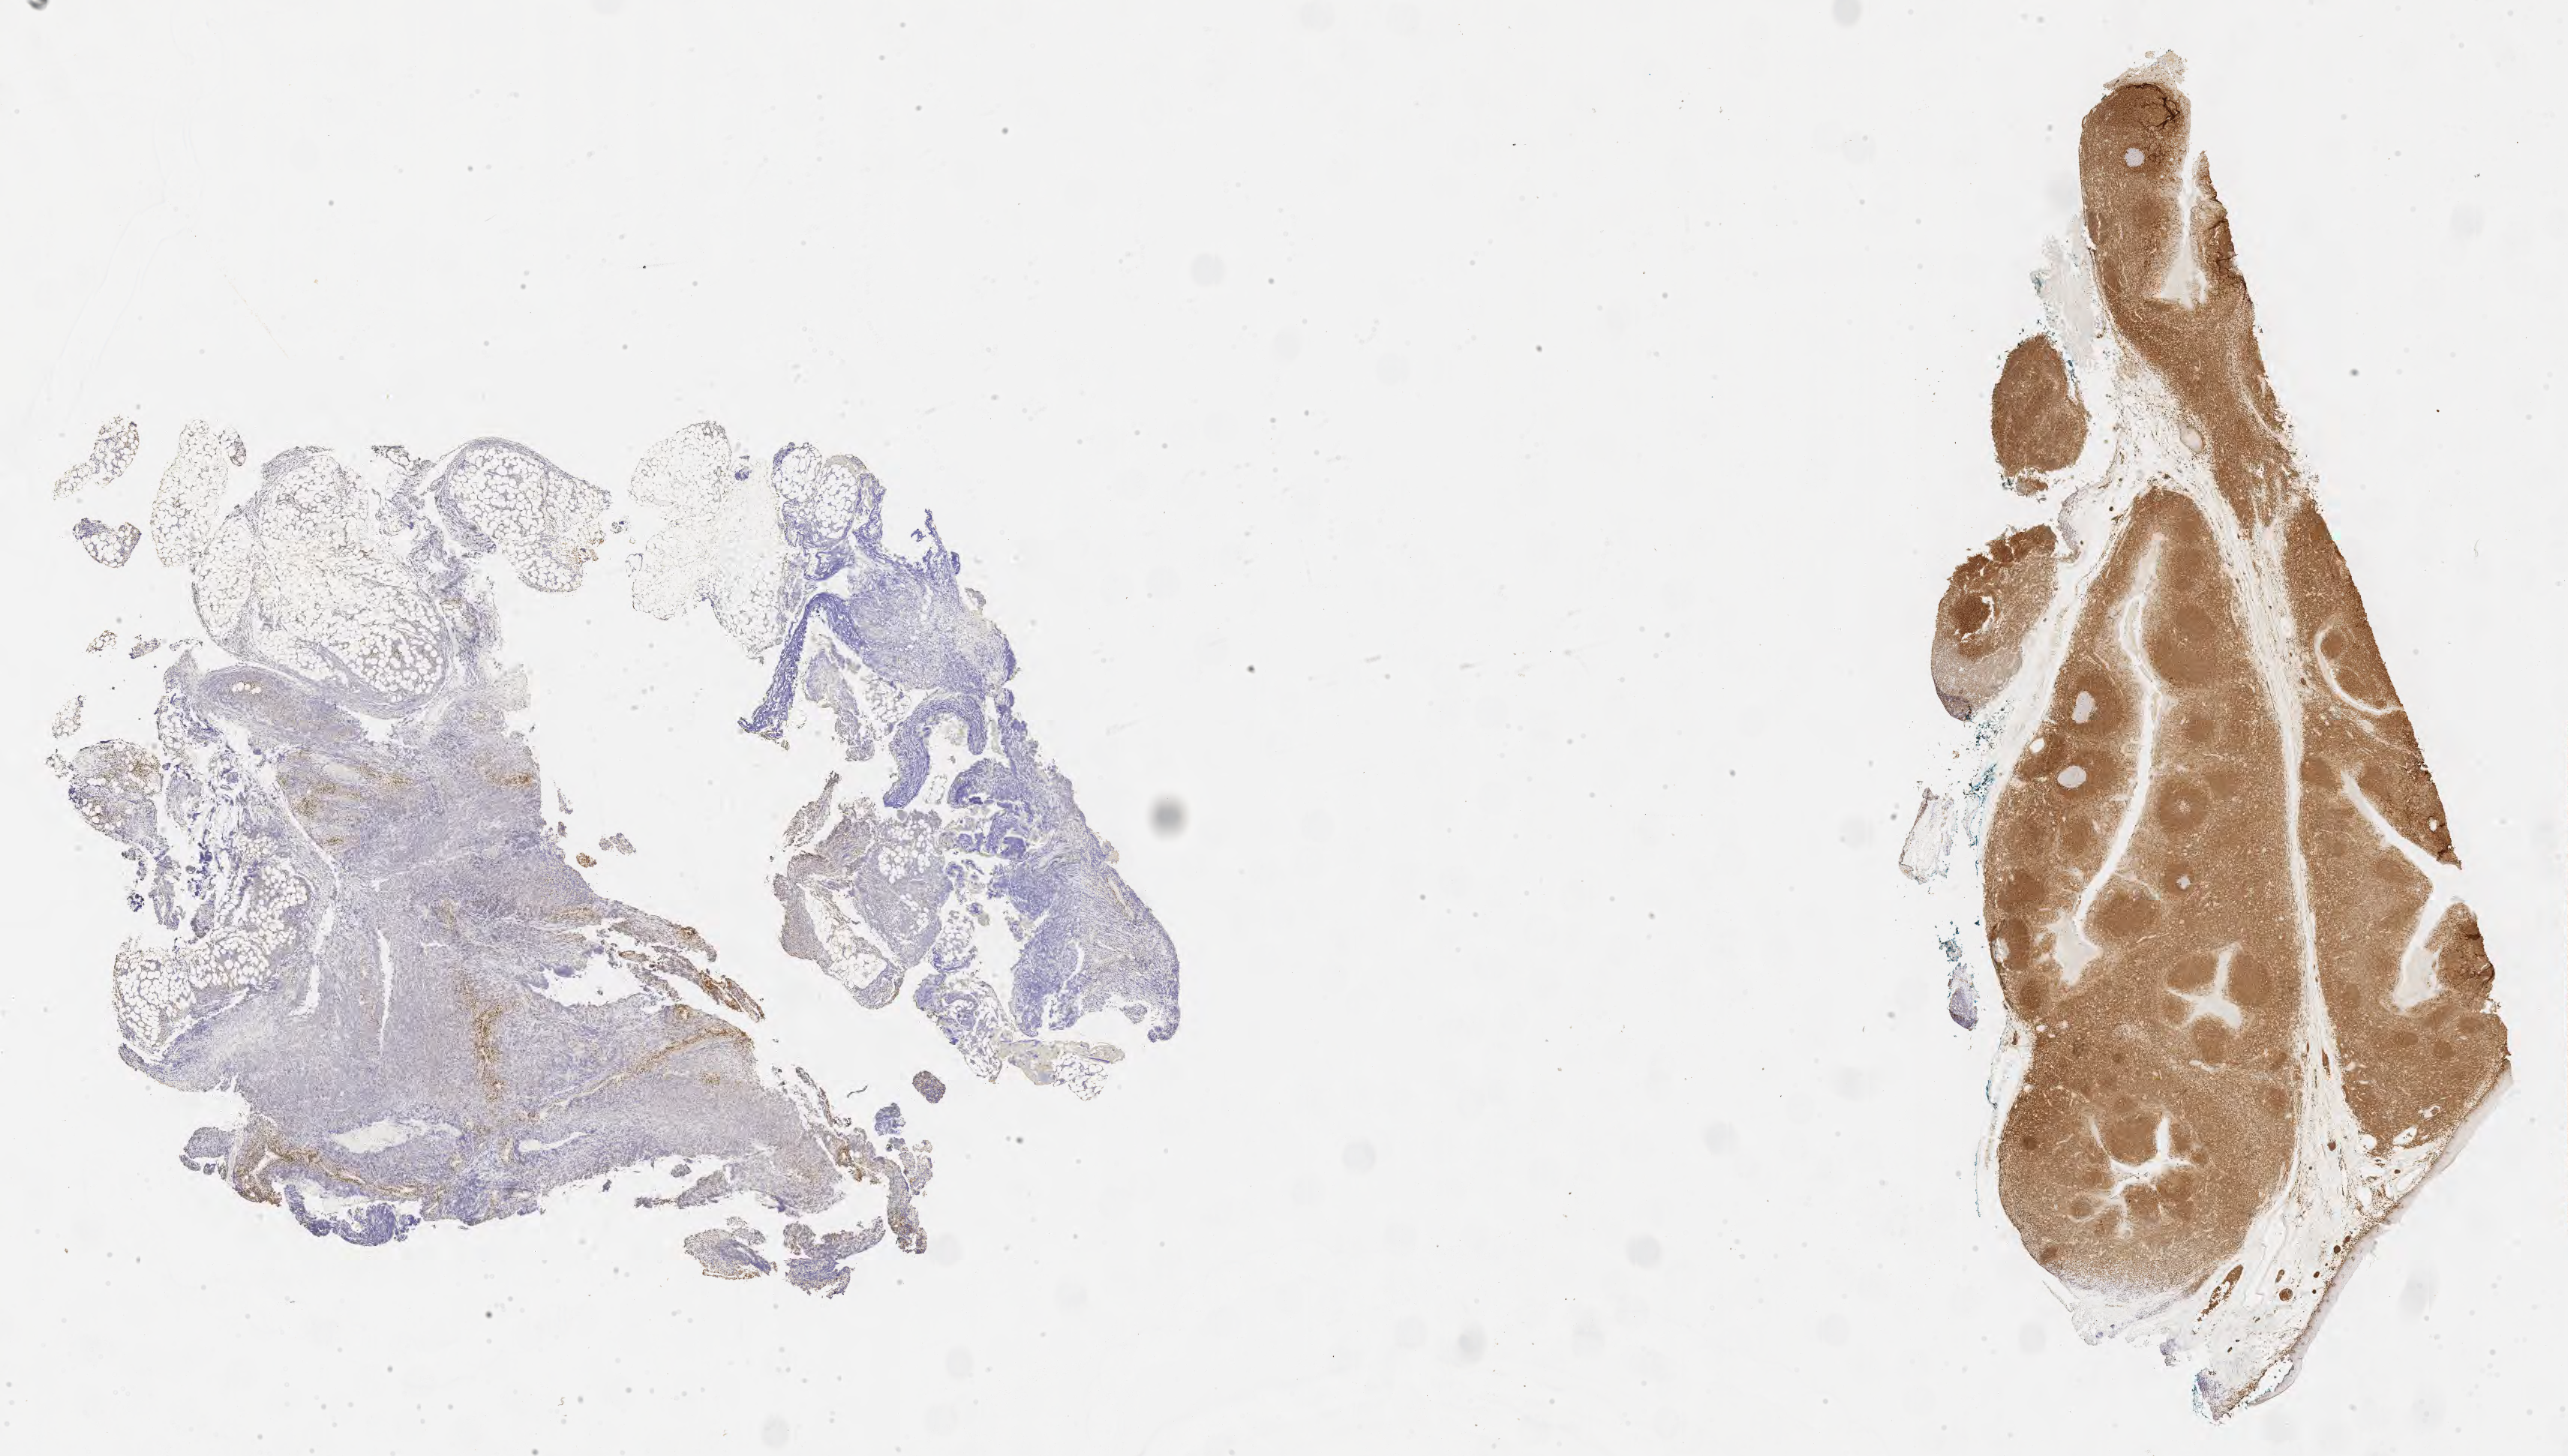
IHC for BCL2, whole-slide image, shown as a low-resolution overview of the whole scanned area (about 27.7 x 15.7 mm), tumor tissue, anatomic site: abdominal lymph node. Male, age 9 years at initial diagnosis.
Histologic diagnosis: Burkitt lymphoma, NOS.